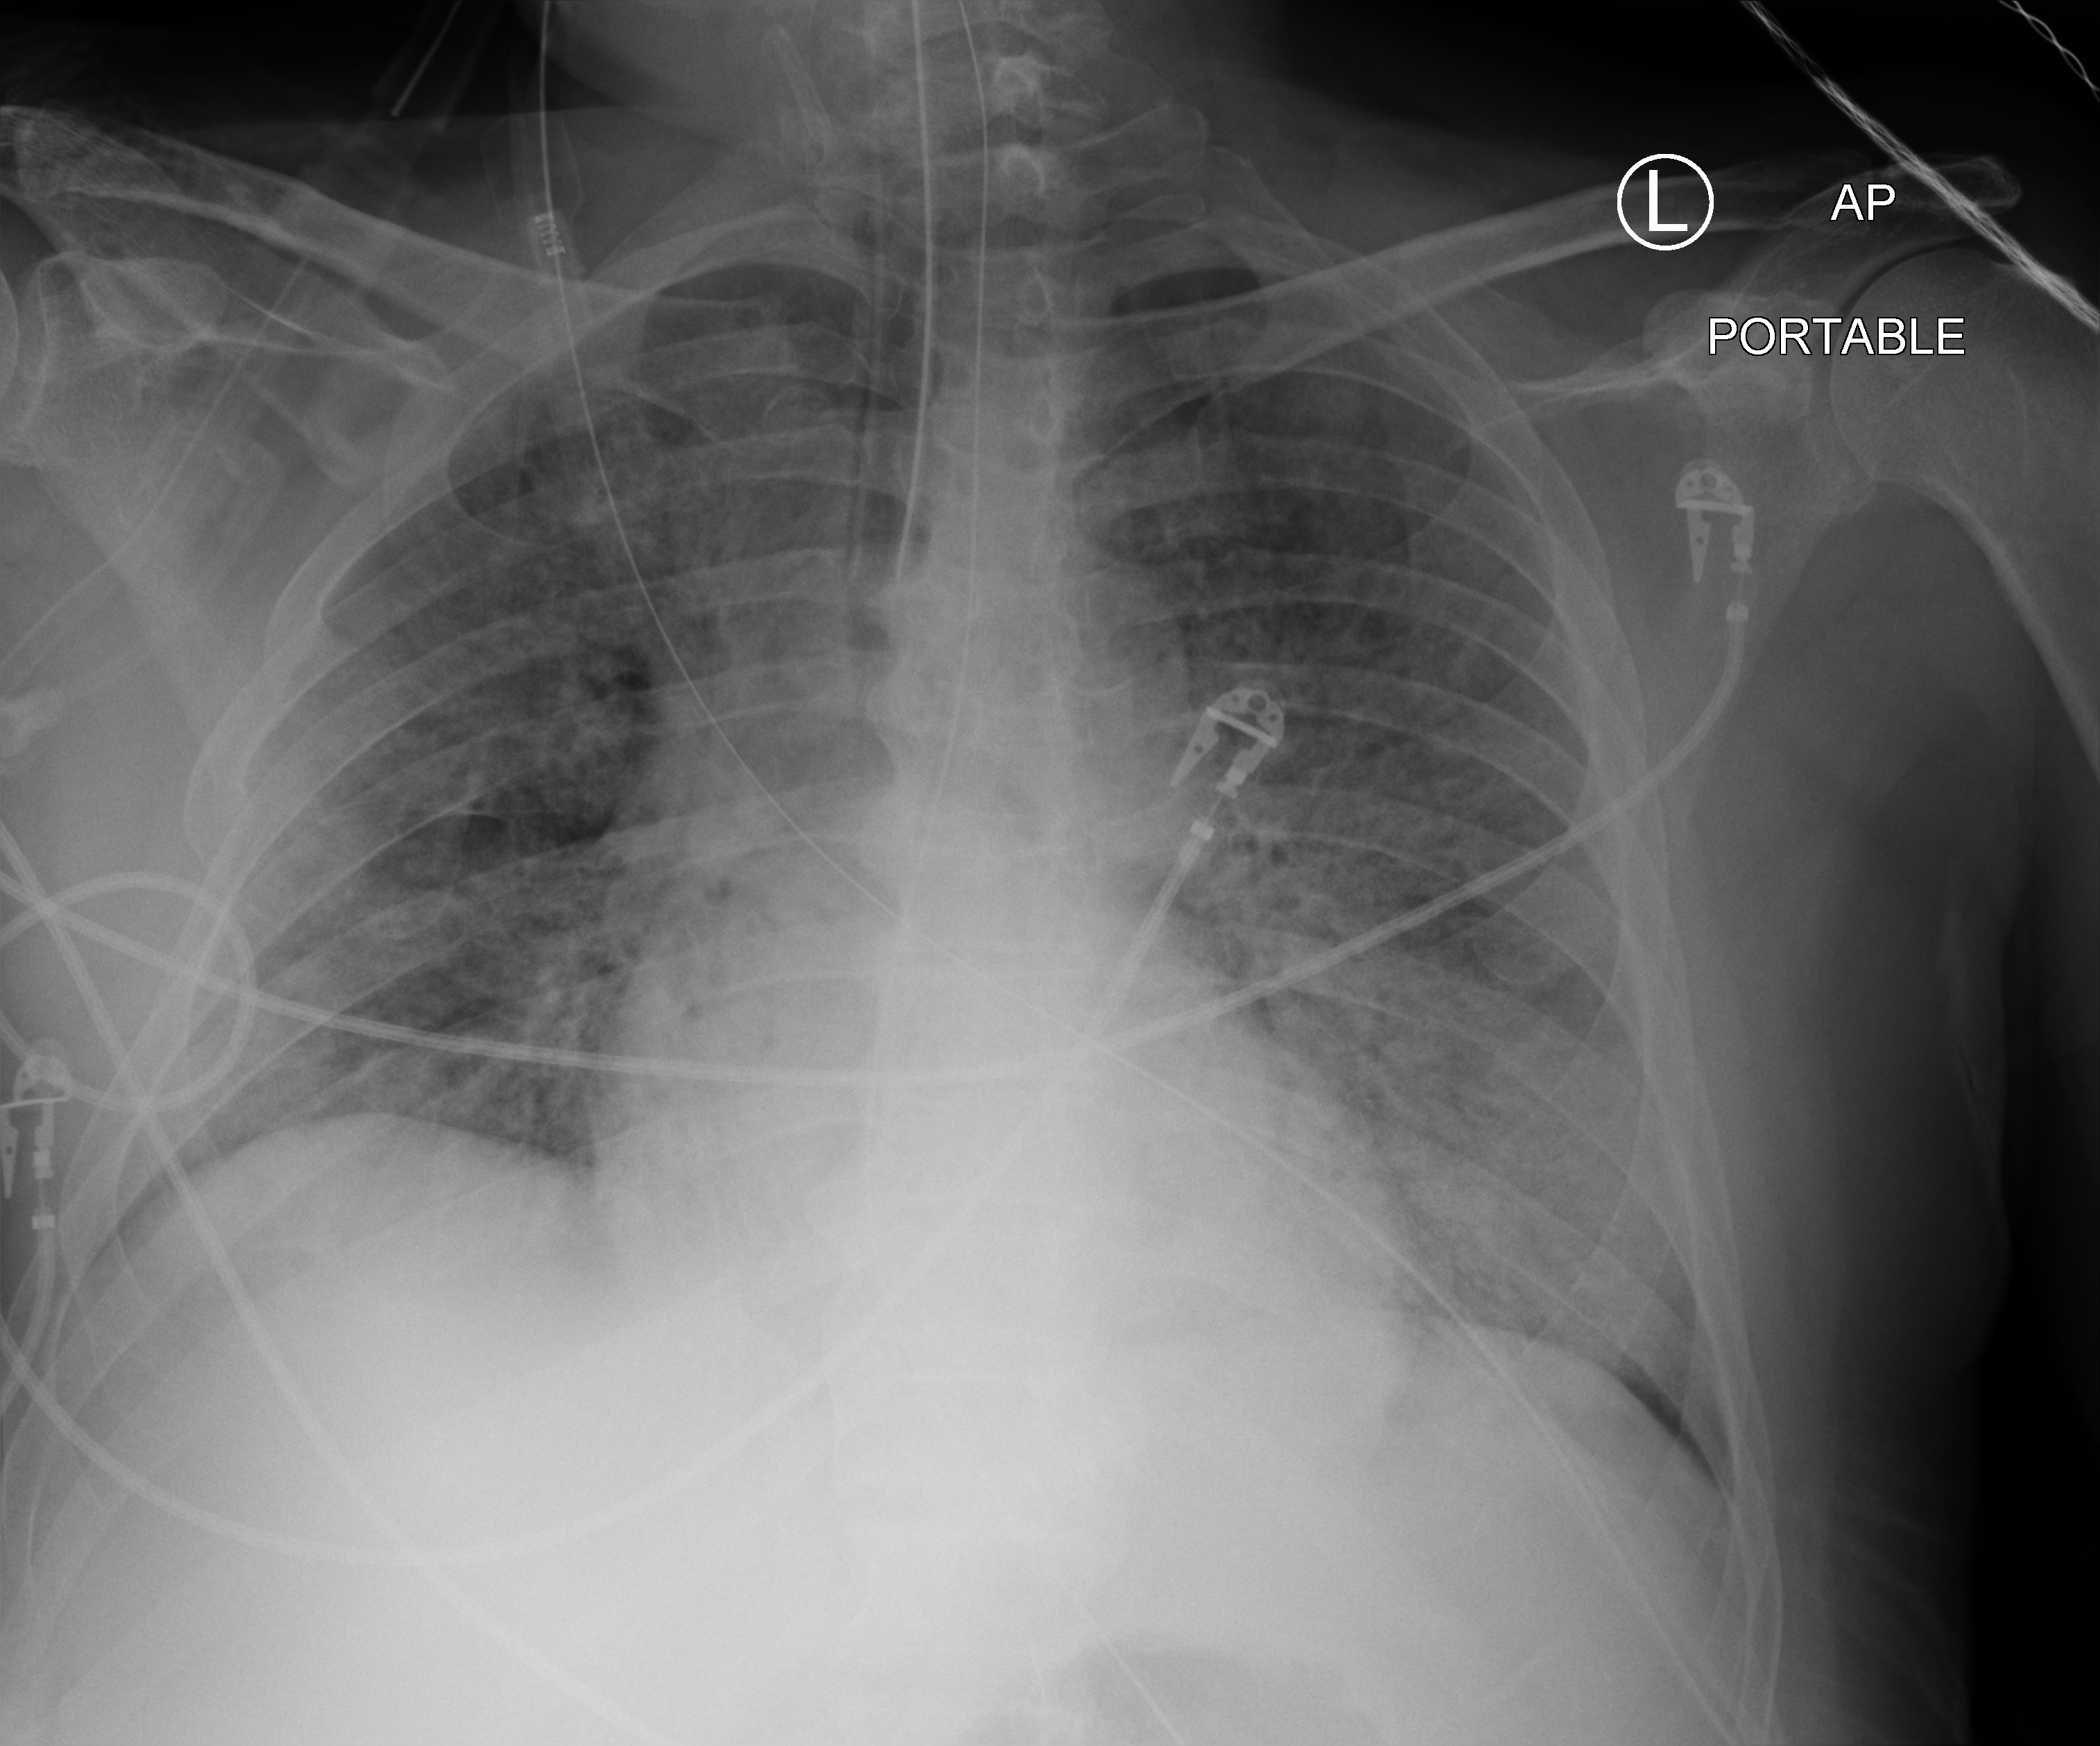
Bedside chest radiograph (computed radiography), anteroposterior (AP) projection. Male patient hospitalised with COVID-19, age 60–74 years.
Admission-level facts for this patient (not findings on this image; timing relative to this image not recorded): mechanically ventilated during this hospital stay: yes.